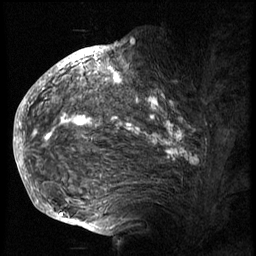
Breast MRI (dynamic contrast-enhanced), one sagittal slice. Position 47 of 74 along the scan axis. 3 images stored at this slice position (order not interpretable as contrast timing). 1.5 T. TE 4.2 ms, TR 8.9 ms. 256 × 256 image matrix. Female patient, age 57 years. Case-level facts recorded for this patient, not image findings: setting: breast cancer imaged before/during neoadjuvant chemotherapy; receptor status: HER2-positive.
Outlined on this slice (semi-automatically segmented with operator editing):
- analysis volume of interest (the breast-tissue region the enhancement analysis was run in; not a lesion): bounding box (x1, y1, x2, y2) in pixels: (40, 62, 236, 175)
- tumour enhancement mask (voxels above the 140 % enhancement threshold inside the analysis volume of interest): (45, 63, 186, 160)